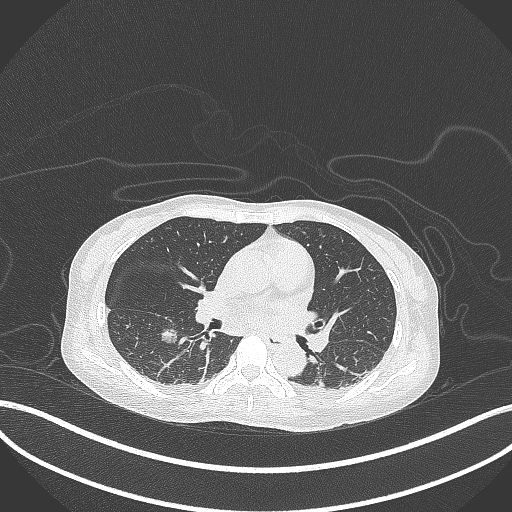
Chest CT, one axial slice; position 162 of 261 along the scan axis; reconstruction kernel B70f; lung window (W 1500 / L -600 HU); 1 mm slice thickness; 512 × 512 image matrix. Female patient, age 44 years. From the clinical record (not read from this slice): clinical TNM (as recorded): T1c N0 M0.
Structures marked on this image (rectangle marked by the reading radiologist):
- lung tumour (recorded histology: adenocarcinoma): bounding box (x1, y1, x2, y2) in pixels: (159, 325, 180, 347)